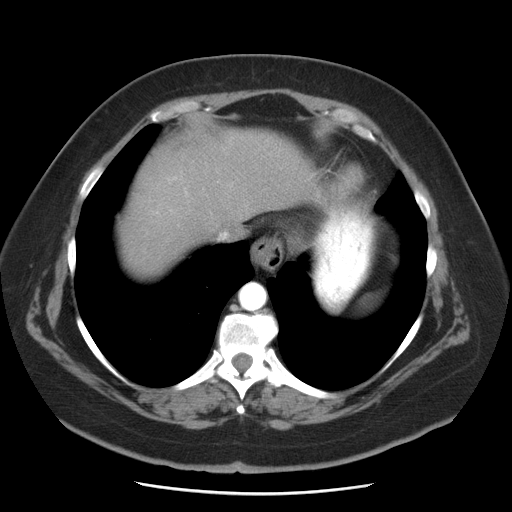
Contrast-enhanced abdominal CT, one axial slice. Position 42 of 55 along the scan axis. Reconstruction kernel STANDARD. Intravenous contrast given. Soft-tissue window (W 400 / L 40 HU). 512 × 512 image matrix, field of view 380 × 380 mm. Female patient, age 52 years. Case-level facts recorded for this patient, not image findings: diagnosis: colorectal cancer liver metastases, imaged before liver resection; multiple liver metastases: yes; largest metastasis: 2.5 cm; disease in both lobes: yes.
Annotated regions visible in this slice (expert manual segmentation):
- liver: bounding box (x1, y1, x2, y2) in pixels: (117, 129, 312, 280)
- planned liver remnant (the part of the liver to remain after resection): (117, 181, 192, 280)